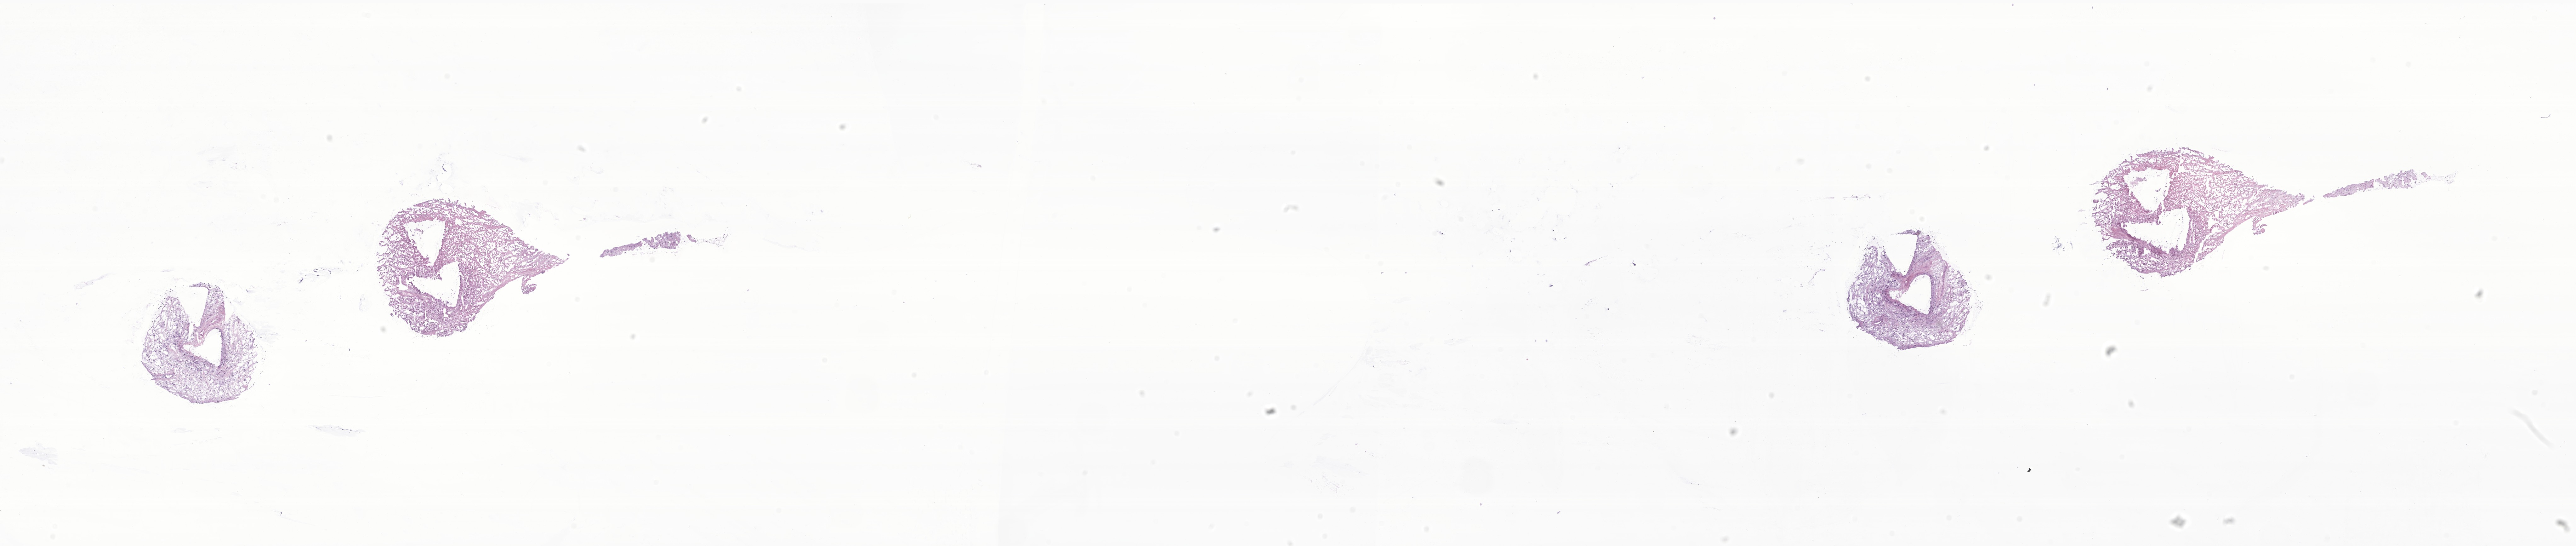
Digitized H&E-stained section of tumor tissue from the soft tissue of pelvis — whole scanned area (about 34.5 x 7.3 mm) shown as a low-resolution overview. Cryosection (OCT / tissue freezing medium). Male patient, age 184 months (15 years 4 months).
Recorded diagnosis: Alveolar rhabdomyosarcoma. Tissue or organ of origin (case record): connective, subcutaneous and other soft tissues of pelvis.